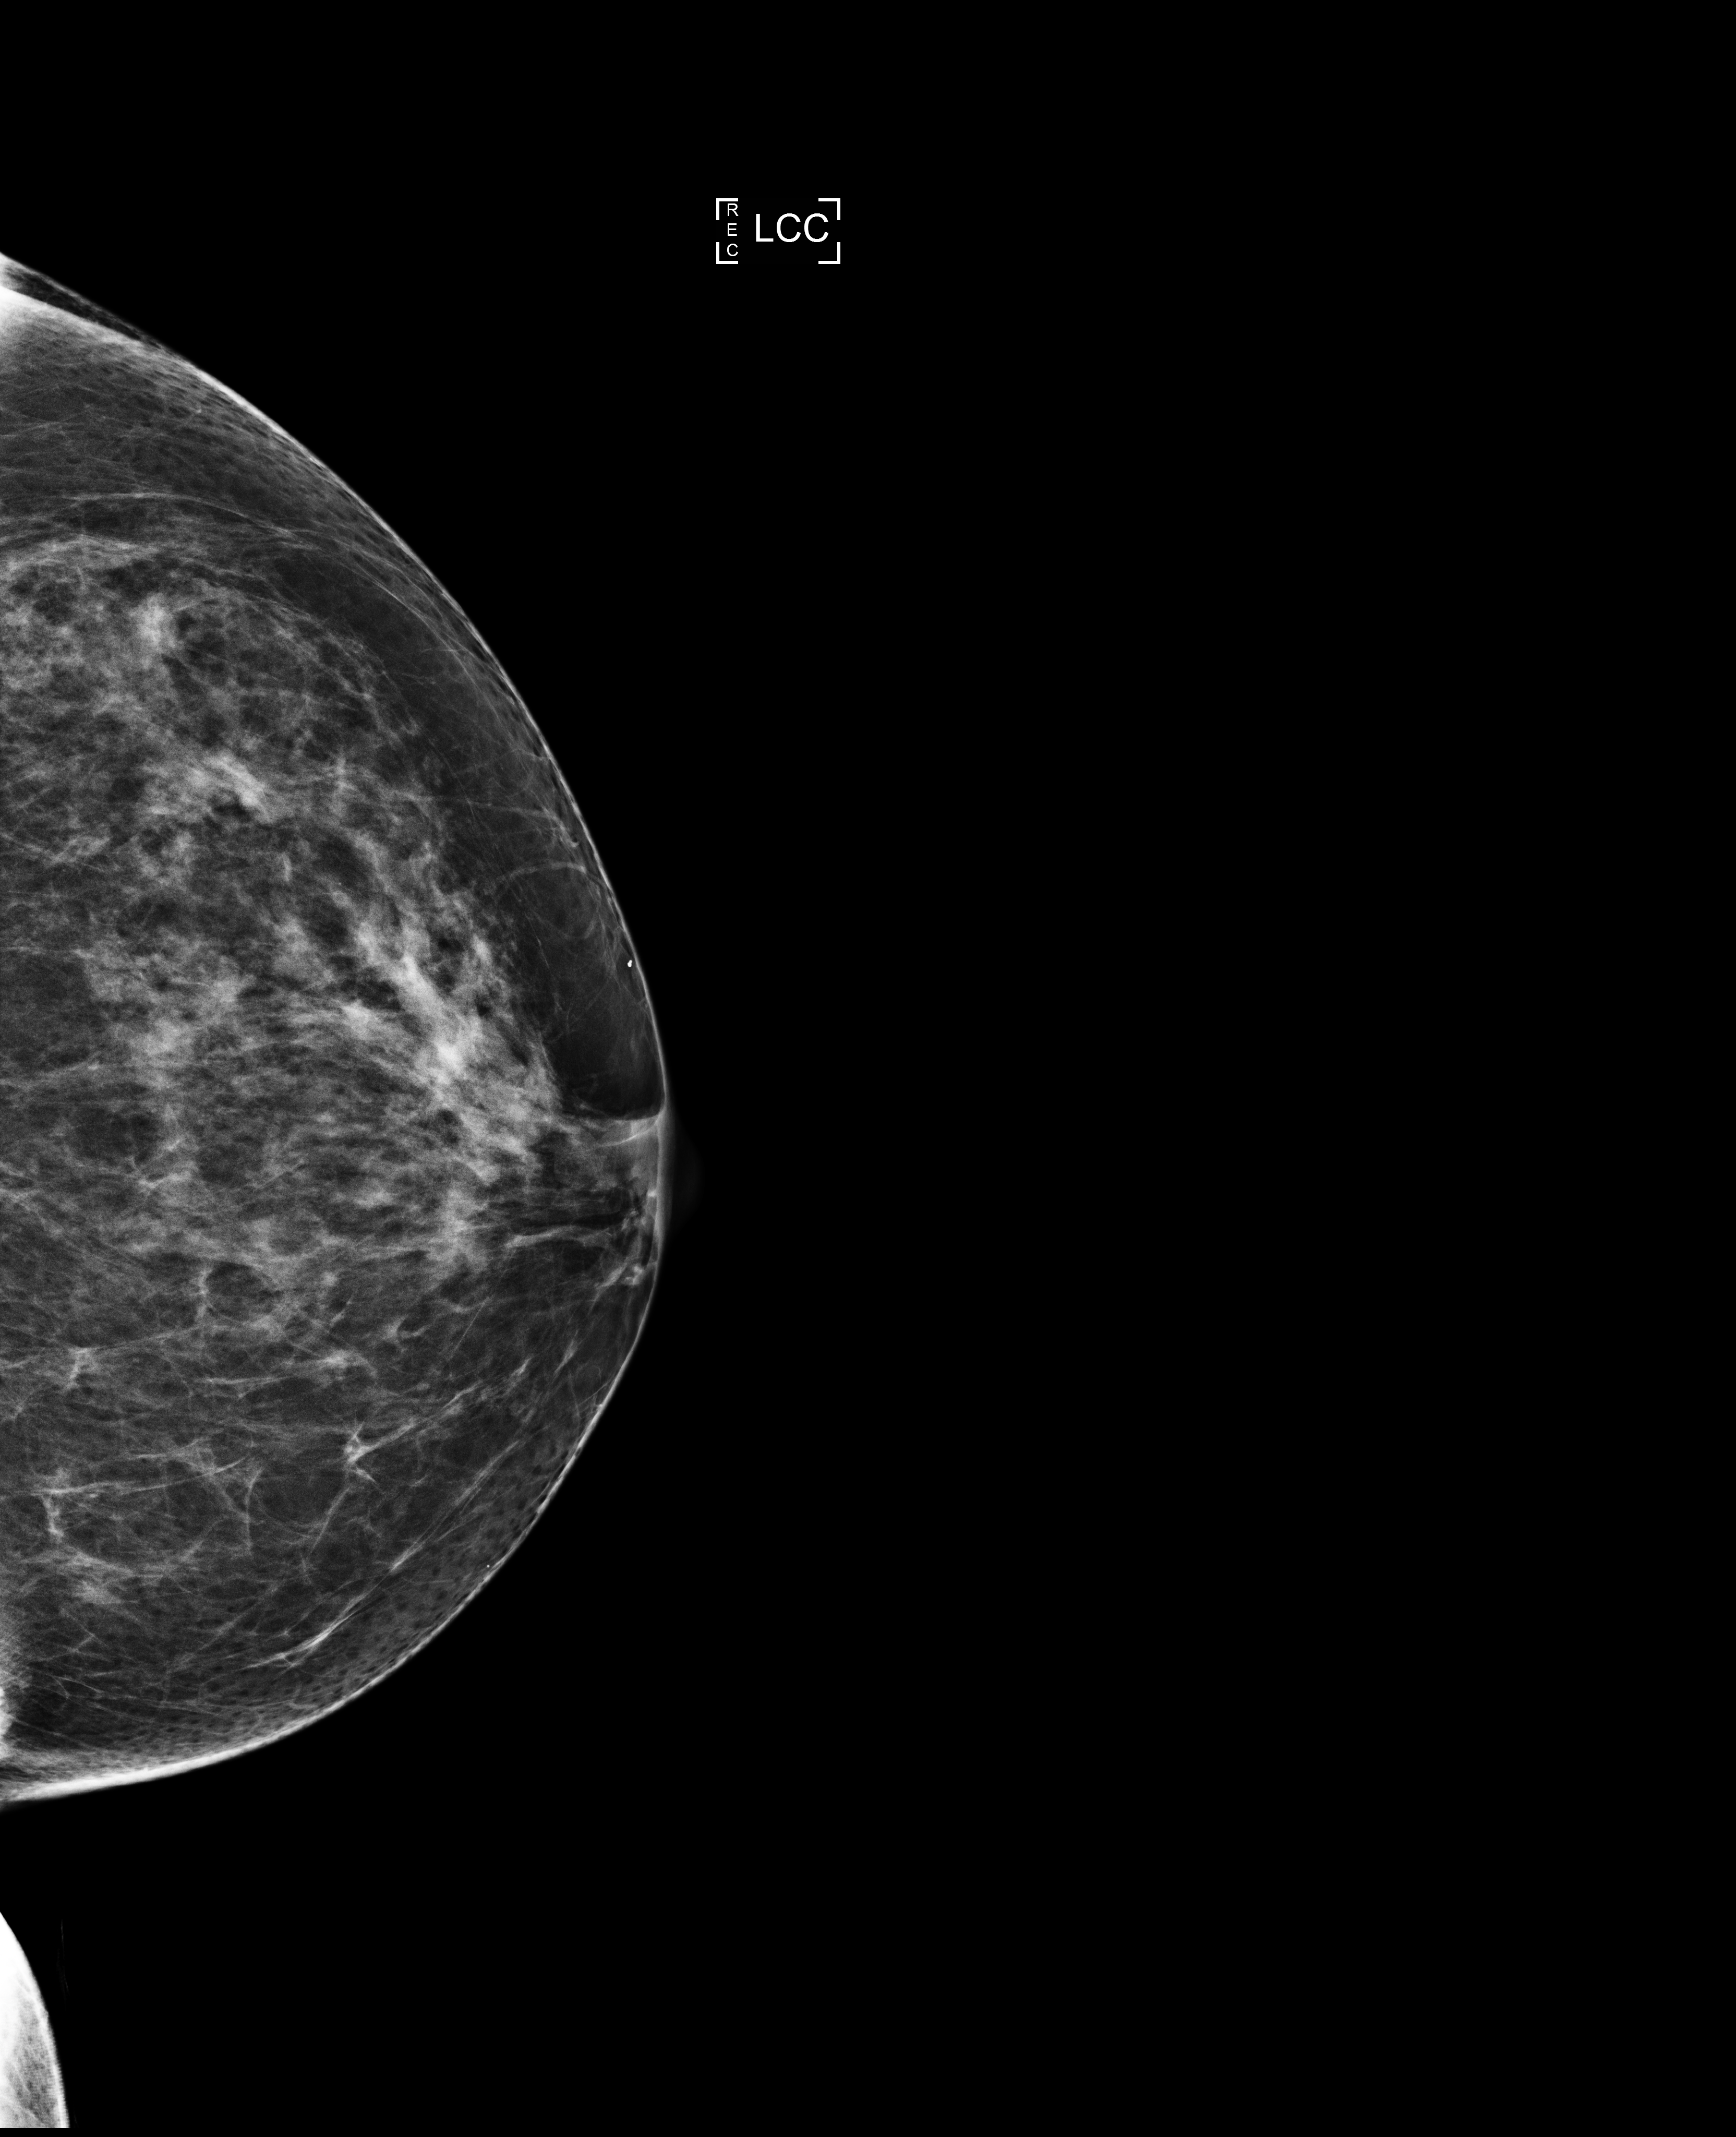
Screening examination, system: Selenia Dimensions. Female patient, age 53 years.
Image type: full-field digital mammogram. Breast: left. Projection: craniocaudal (CC) view.